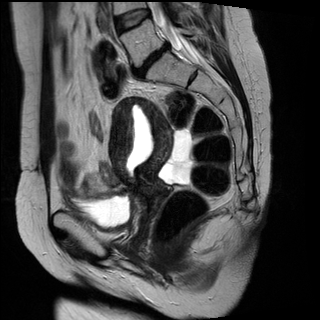
Pelvic MRI for cervical cancer, one sagittal slice. Position 17 of 29 along the scan axis. T2-weighted. 1.5 T. TE 89 ms, TR 2930 ms. 320 × 320 image matrix, field of view 260 × 260 mm. Patient: female, 45 years.
Structures marked on this image (outlined manually by an expert reader):
- uterus and cervix: bounding box <107,95,174,209> (left, top, right, bottom; pixels)